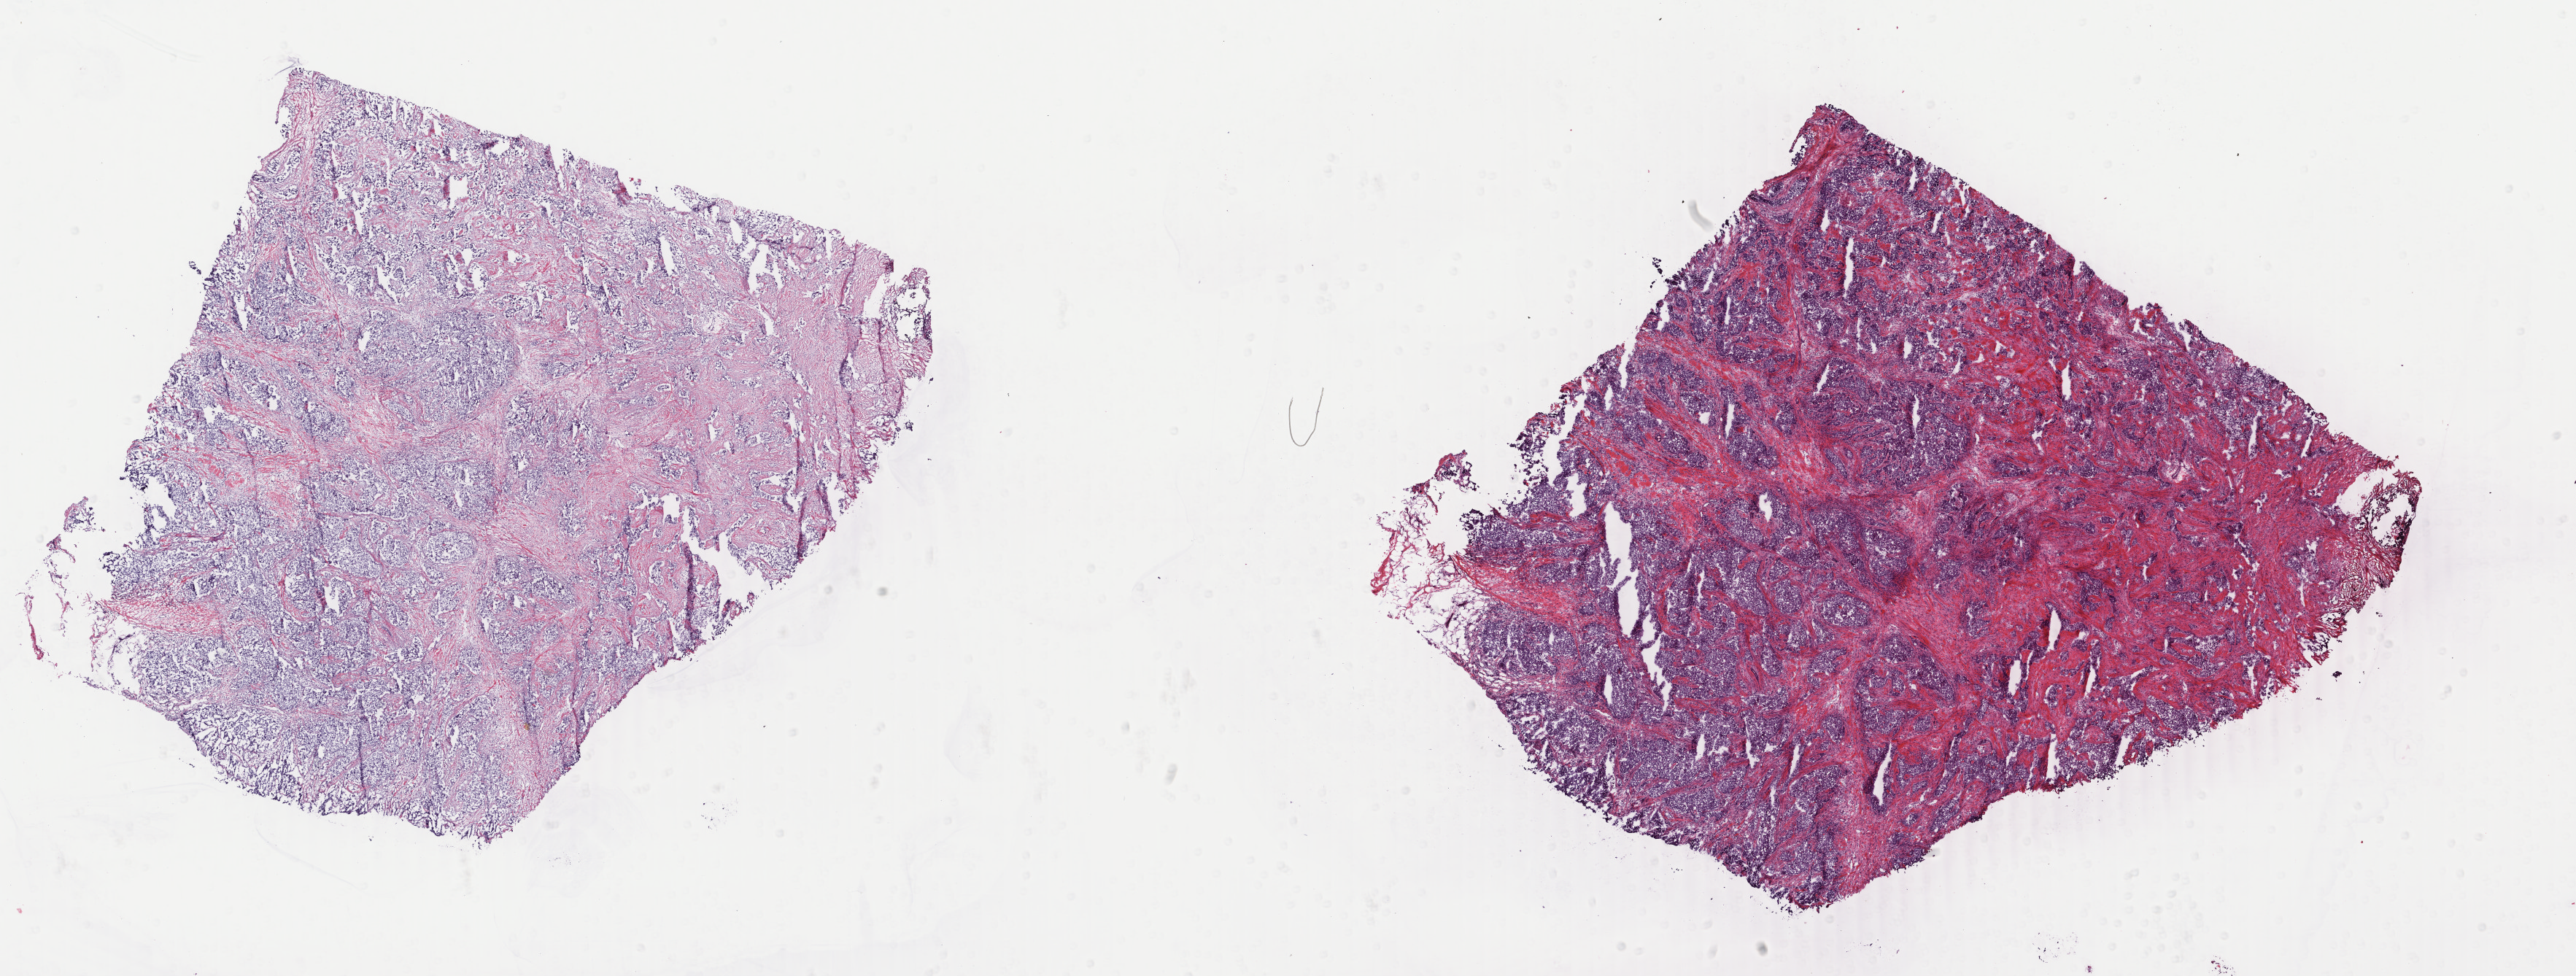
Whole-slide histology image, H&E-stained — whole scanned area (about 28.1 x 10.6 mm, acquisition: 40x scan) shown as a low-resolution overview, frozen section, primary tumour sample from the breast. Patient: female, age at initial diagnosis 52 years. Pathologist review of this section (percent, as recorded): tumour cells 90%, tumour nuclei 80%, normal cells 0%, stromal cells 8%, necrosis 2%. Infiltration values recorded for this section: lymphocyte infiltration 0%, monocyte infiltration 0%, neutrophil infiltration 0%.
- histologic diagnosis: Infiltrating duct carcinoma, NOS
- laterality: left
- AJCC pathologic stage: IIA (6th edition)
- lymph nodes positive (case pathology): 0 of 2 examined